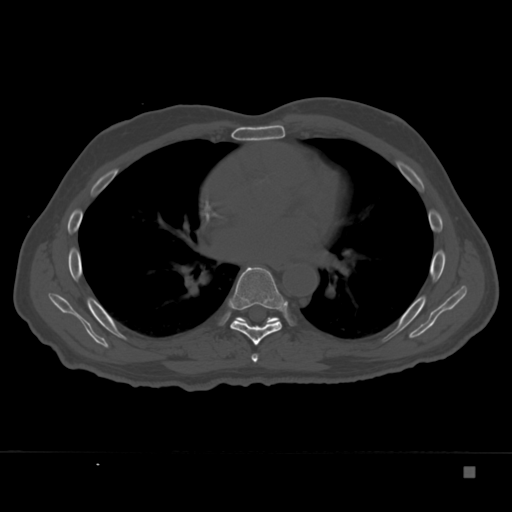
CT including the spine, one axial slice. Slice 221 of 332 in the series (ordered by position). Reconstruction kernel Br40s. Bone window (W 1800 / L 400 HU). 1.5 mm slice thickness. 512 × 512 image matrix, field of view 389 × 389 mm. Male patient, age 72 years. From the clinical record (not read from this slice): primary cancer: skeletal.
Structures marked on this image (semi-automatic segmentation, software-assisted and operator-edited):
- T6 vertebra: bounding box [x1, y1, x2, y2] px = [251, 354, 258, 362]
- T7 vertebra: [230, 267, 284, 346]
- T8 vertebra: [235, 317, 280, 323]